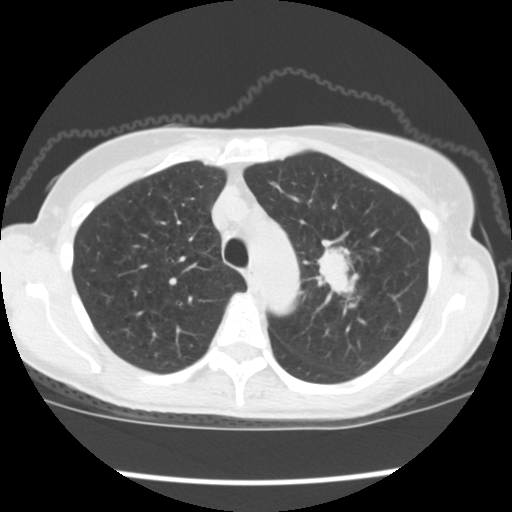
Low-dose screening chest CT, one axial slice; position 138 of 176 along the scan axis; lung window (W 1500 / L -600 HU); 2.5 mm slice thickness; 512 × 512 image matrix.
Outlined on this slice (expert manual segmentation):
- lesion 1 (tumor, upper lobe of left lung): bounding box [x1, y1, x2, y2] px = [316, 247, 359, 300]